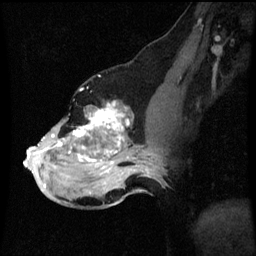
Breast MRI (dynamic contrast-enhanced), one sagittal slice; slice 33 of 60 in the series (ordered by position); dynamic contrast-enhanced series, image 2 of 3 at this slice position (ordered by acquisition); 1.5 T; TE 4.2 ms, TR 8.9 ms; 2 mm slice thickness; 256 × 256 image matrix, field of view 200 × 200 mm. Female patient, age 49 years. From the clinical record (not read from this slice): setting: breast cancer imaged before/during neoadjuvant chemotherapy; receptor status: HR-positive, HER2-negative.
Structures marked on this image (semi-automatic segmentation, software-assisted and operator-edited):
- analysis volume of interest (the breast-tissue region the enhancement analysis was run in; not a lesion): bounding box (x1, y1, x2, y2) in pixels: (24, 102, 159, 199)
- tumour enhancement mask (voxels above the 70 % enhancement threshold inside the analysis volume of interest): (26, 104, 151, 187)